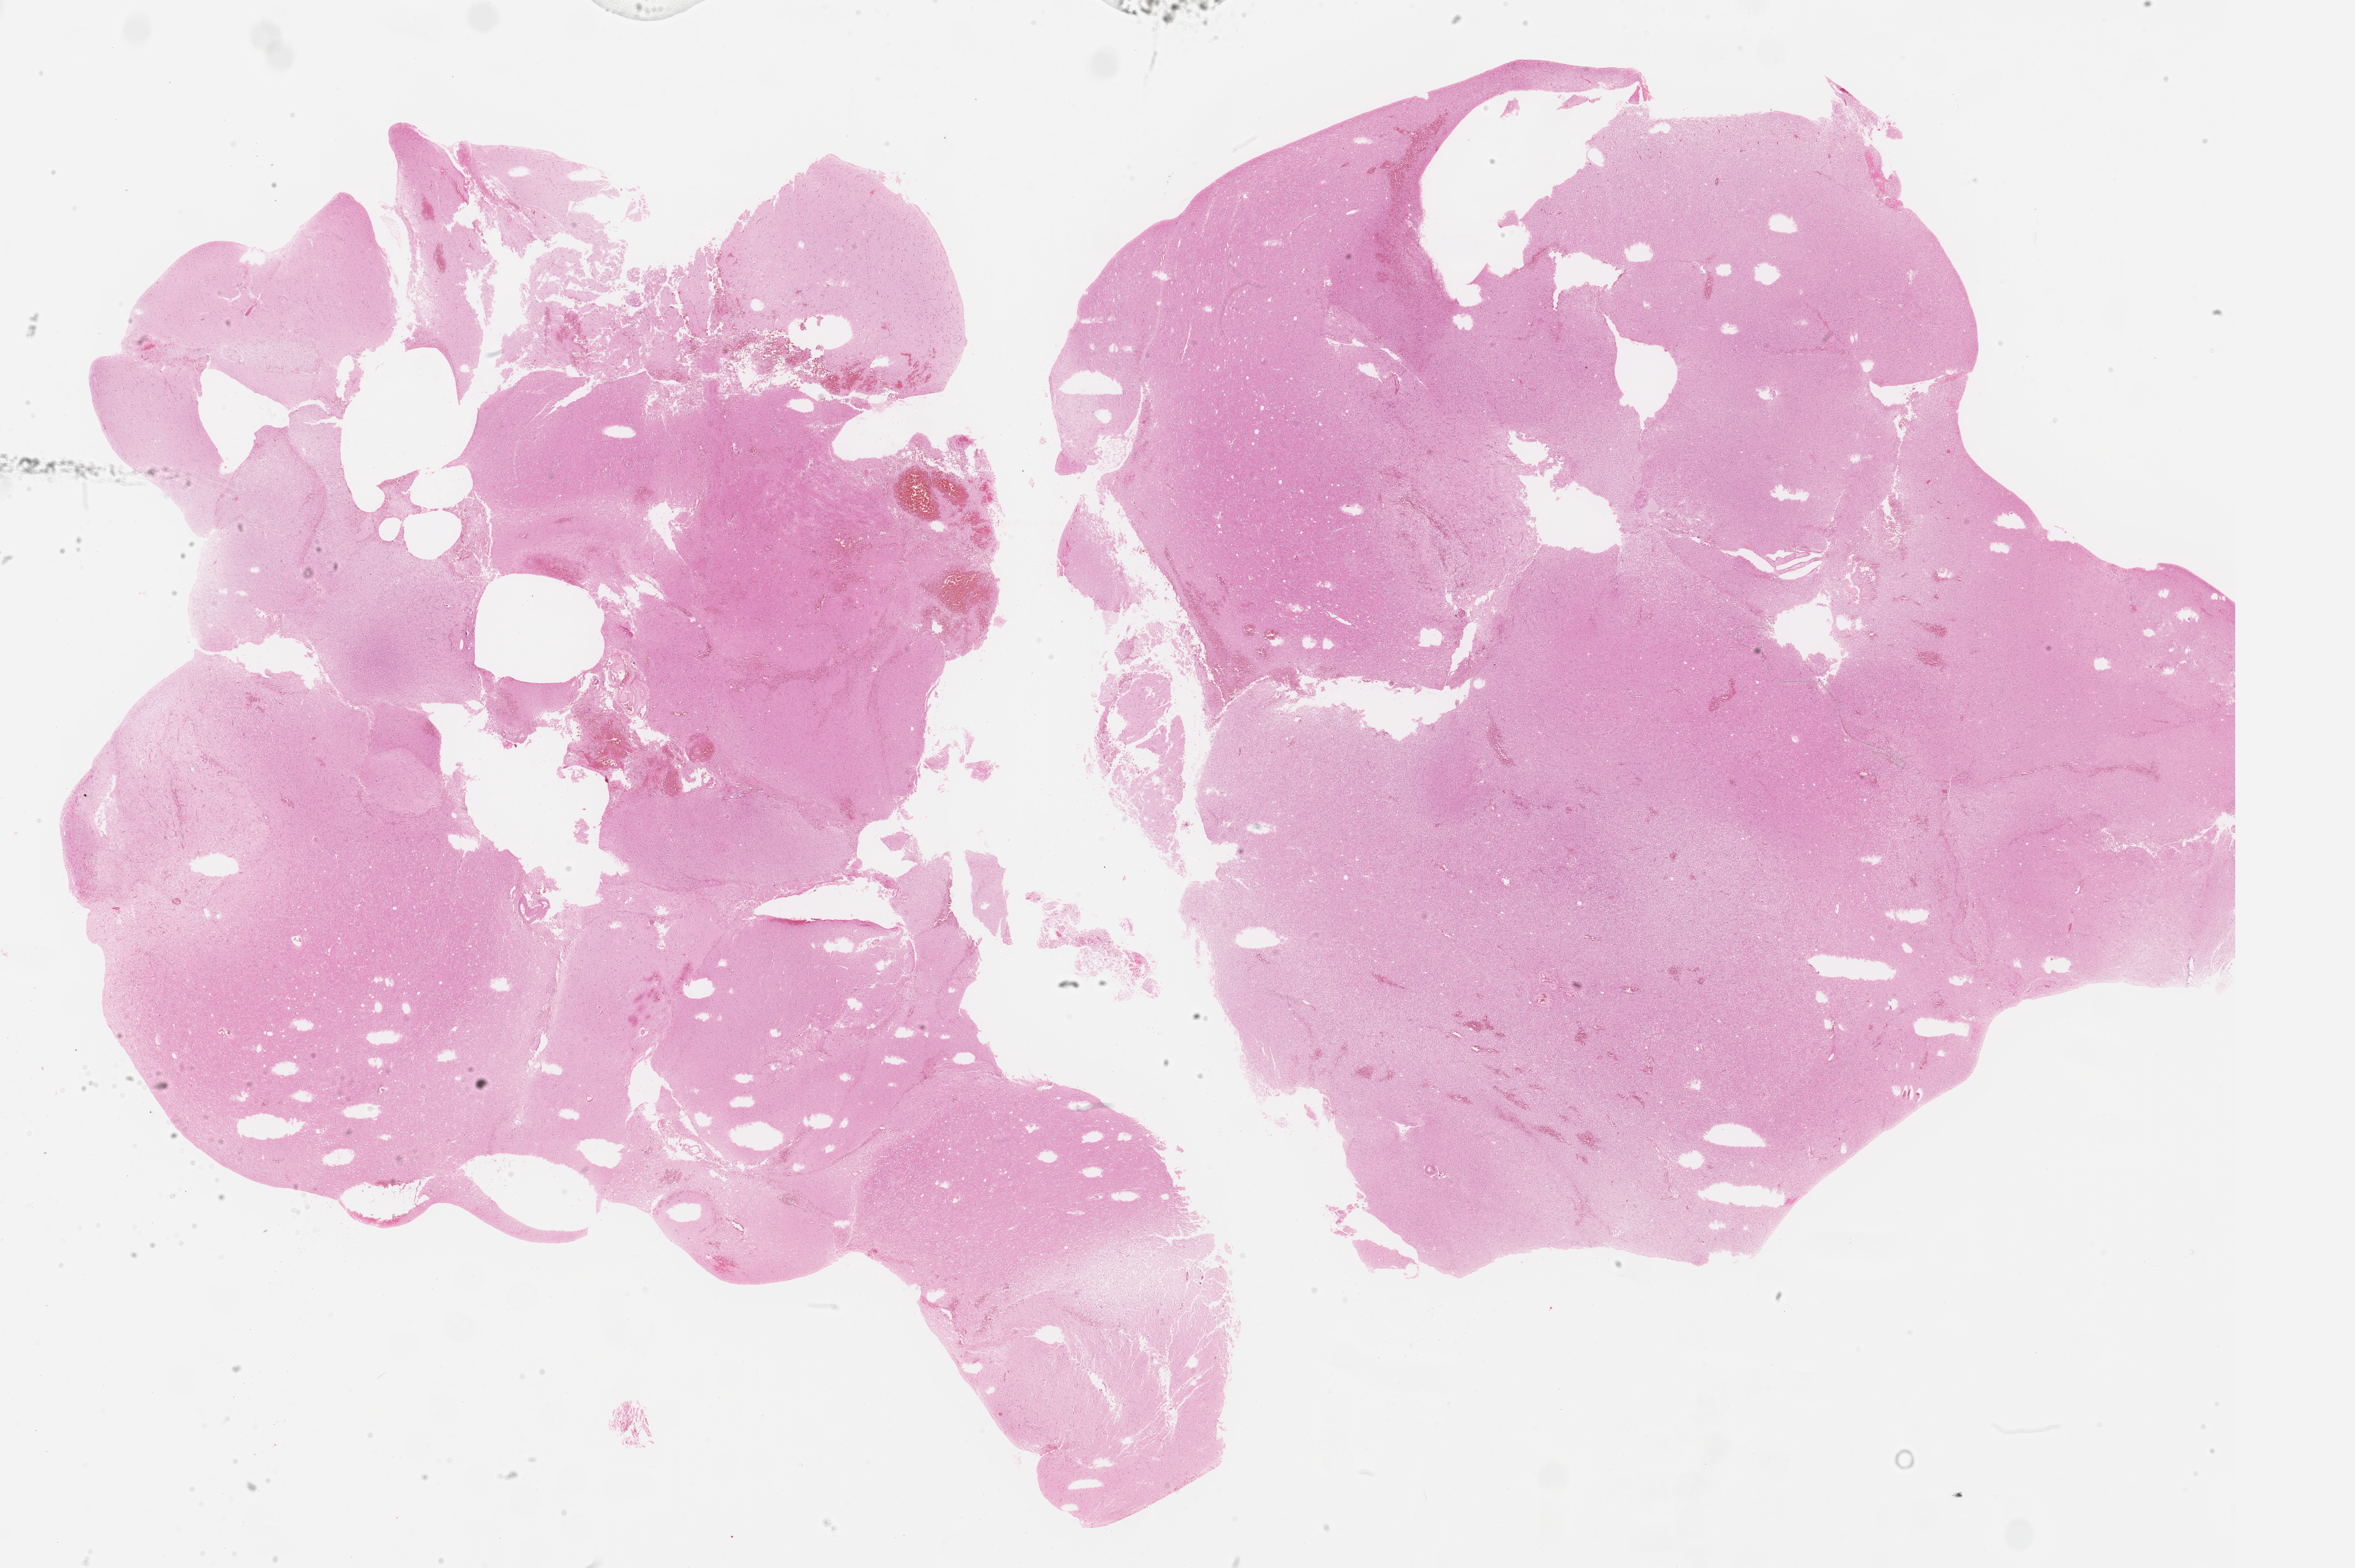
H&E whole-slide image, low-resolution overview of the scanned area, about 28.5 x 19.0 mm (acquisition: 40x scan); FFPE section; brain, primary tumour sample. Male, age 40 years at initial diagnosis. Histologic grade: G2 (moderately differentiated).
Laterality: right. Diagnosis: Oligodendroglioma, NOS.